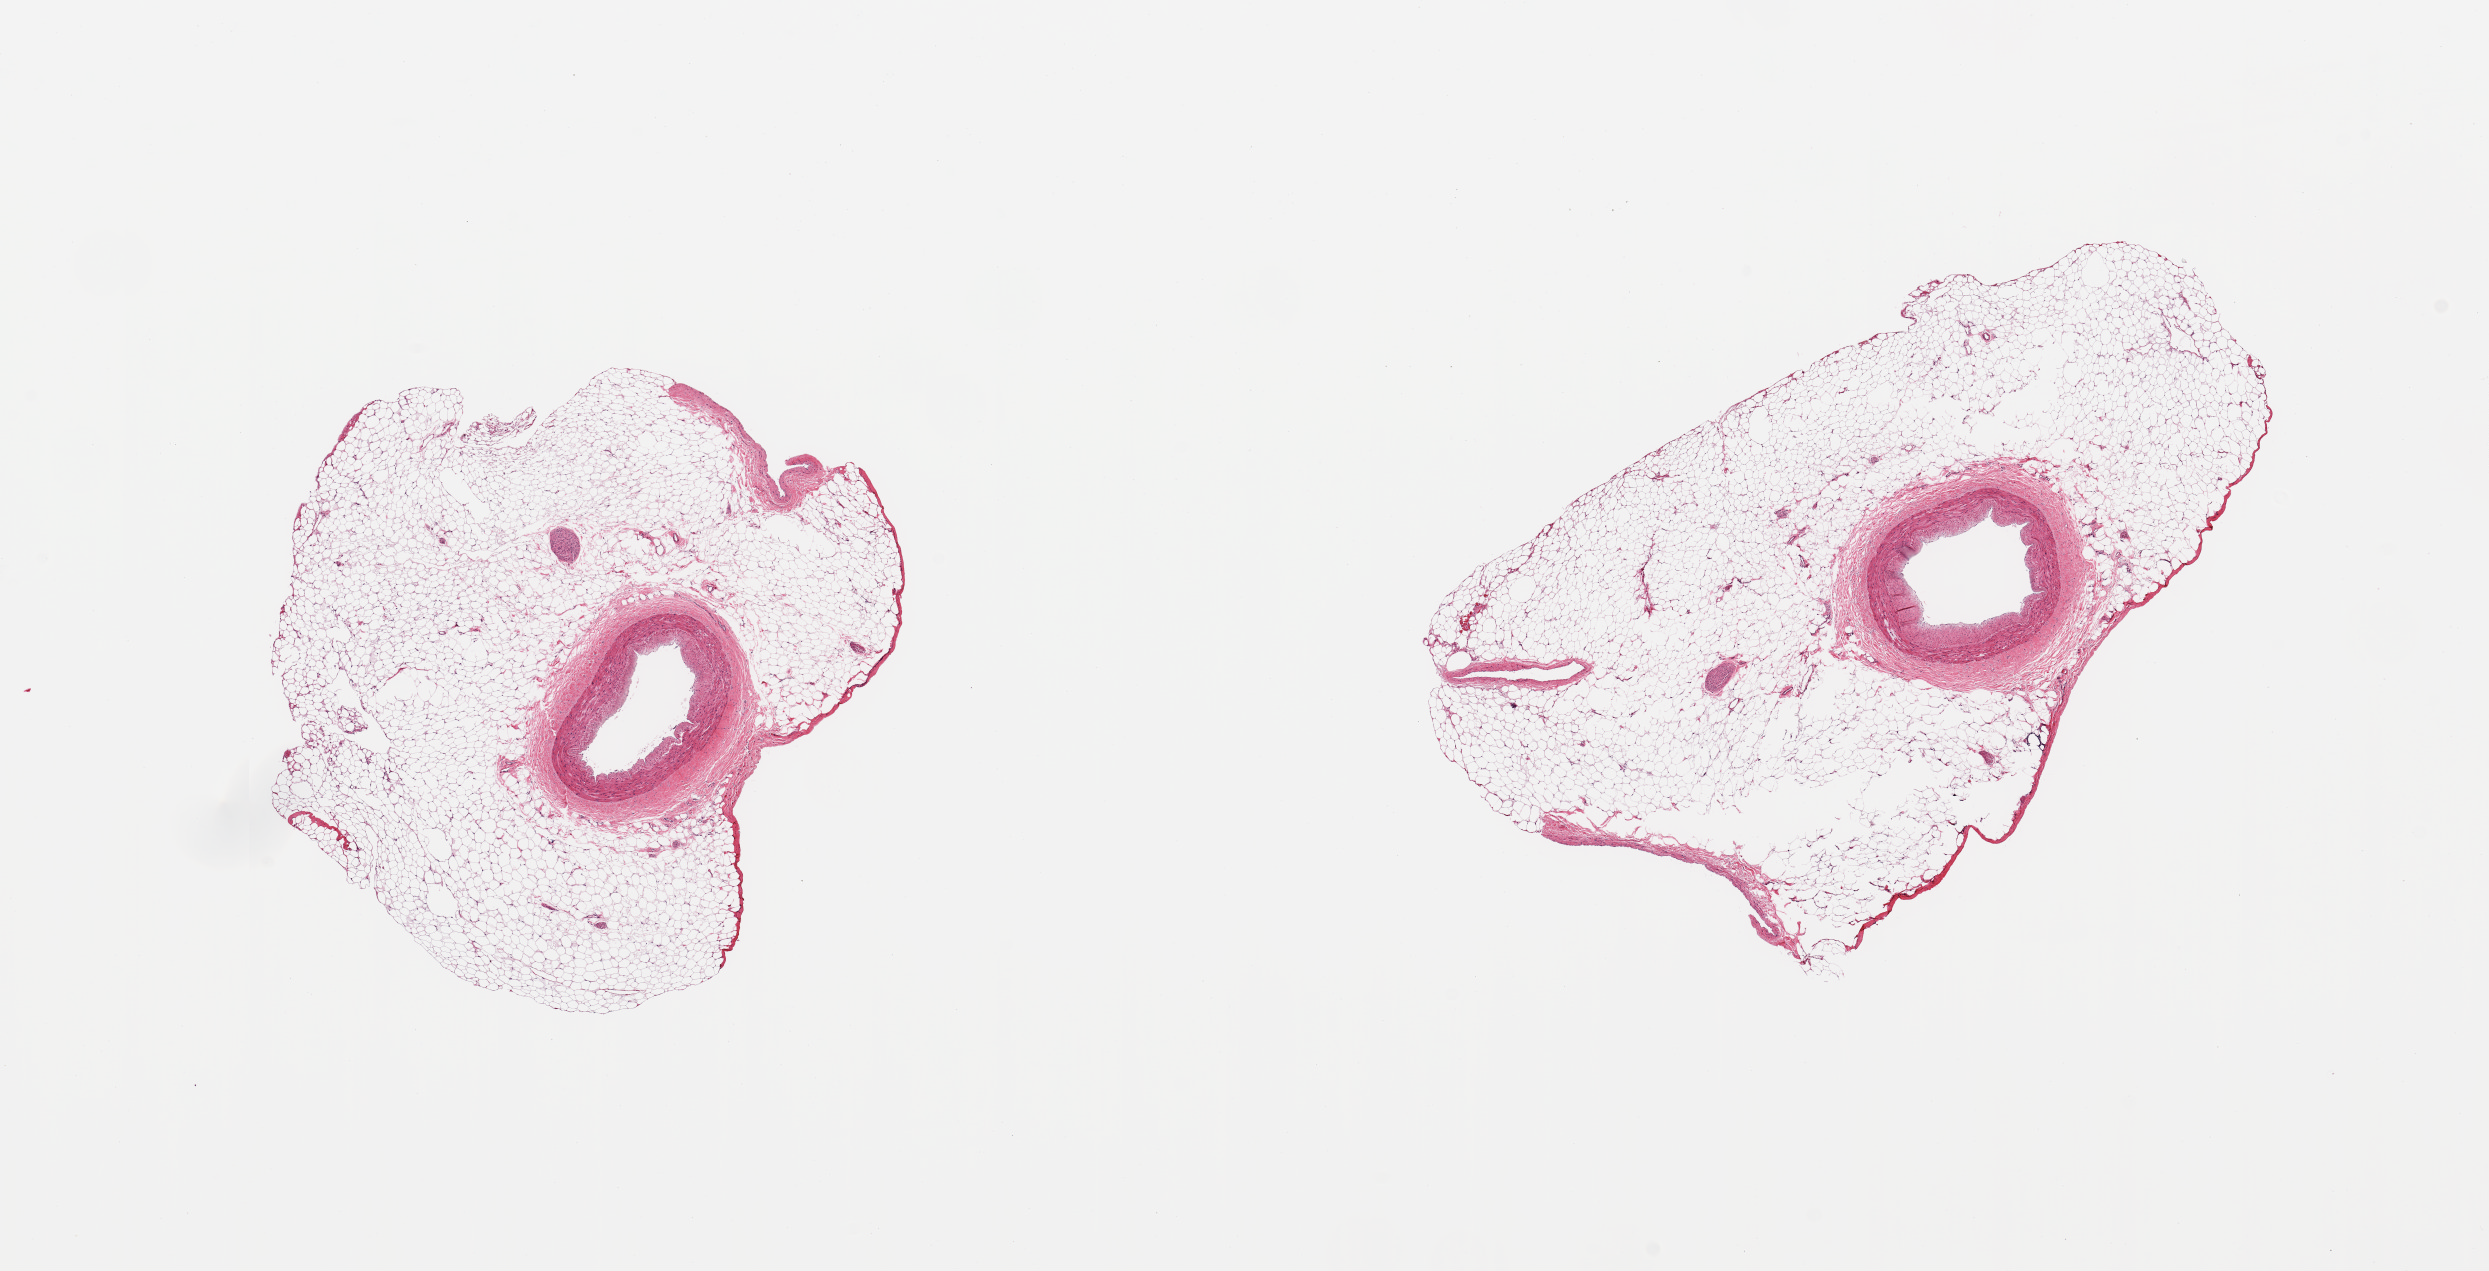
Whole-slide image, hematoxylin and eosin (H&E) stain, brightfield, a low-resolution overview of the entire scanned area, about 19.7 x 10.1 mm; PAXgene-fixed paraffin-embedded (PFPE) section; target tissue: coronary artery; tissue donor sample. Donor: female.
Reviewer comment on this tissue sample: 2 pieces; external fat occupies 90%; minimal plaque.